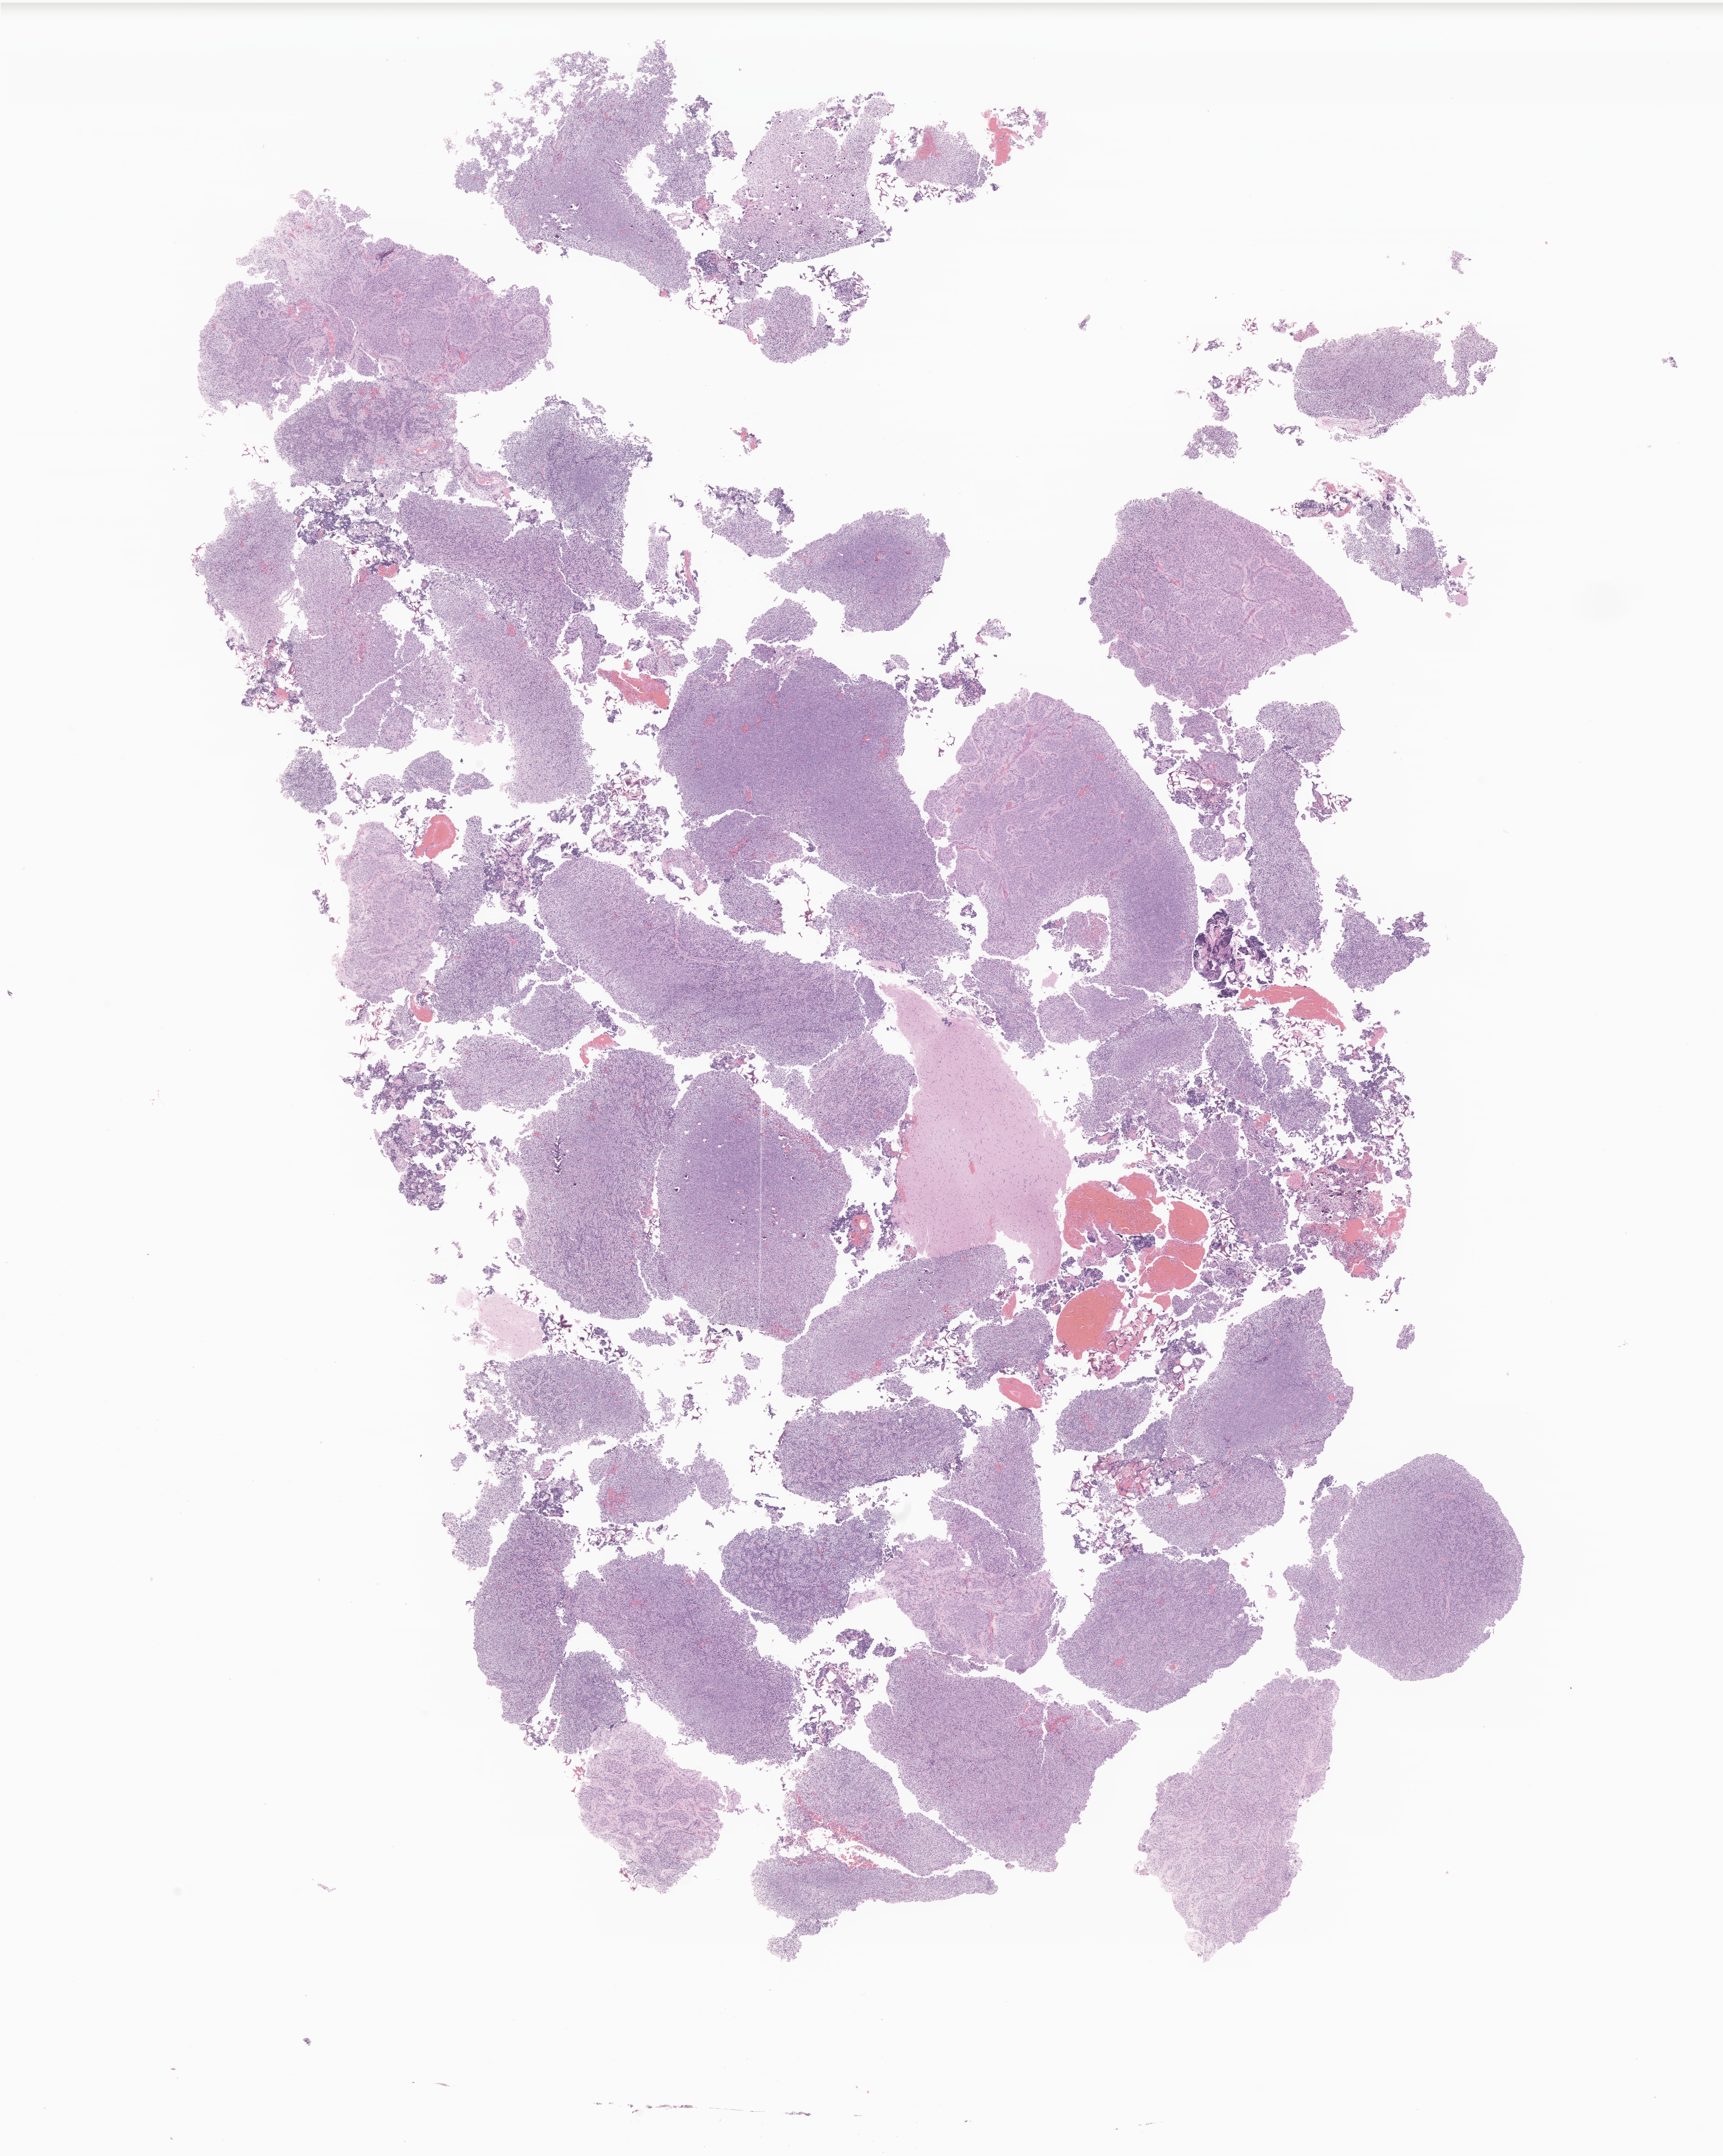
Hematoxylin and eosin (H&E) whole-slide image of tumor tissue from the brain — low-resolution overview of the scanned area, about 17.1 x 21.4 mm, formalin-fixed, paraffin-embedded (FFPE) tissue. Male patient, age 72 months (6 years).
Diagnosis: Neoplasm, uncertain whether benign or malignant.